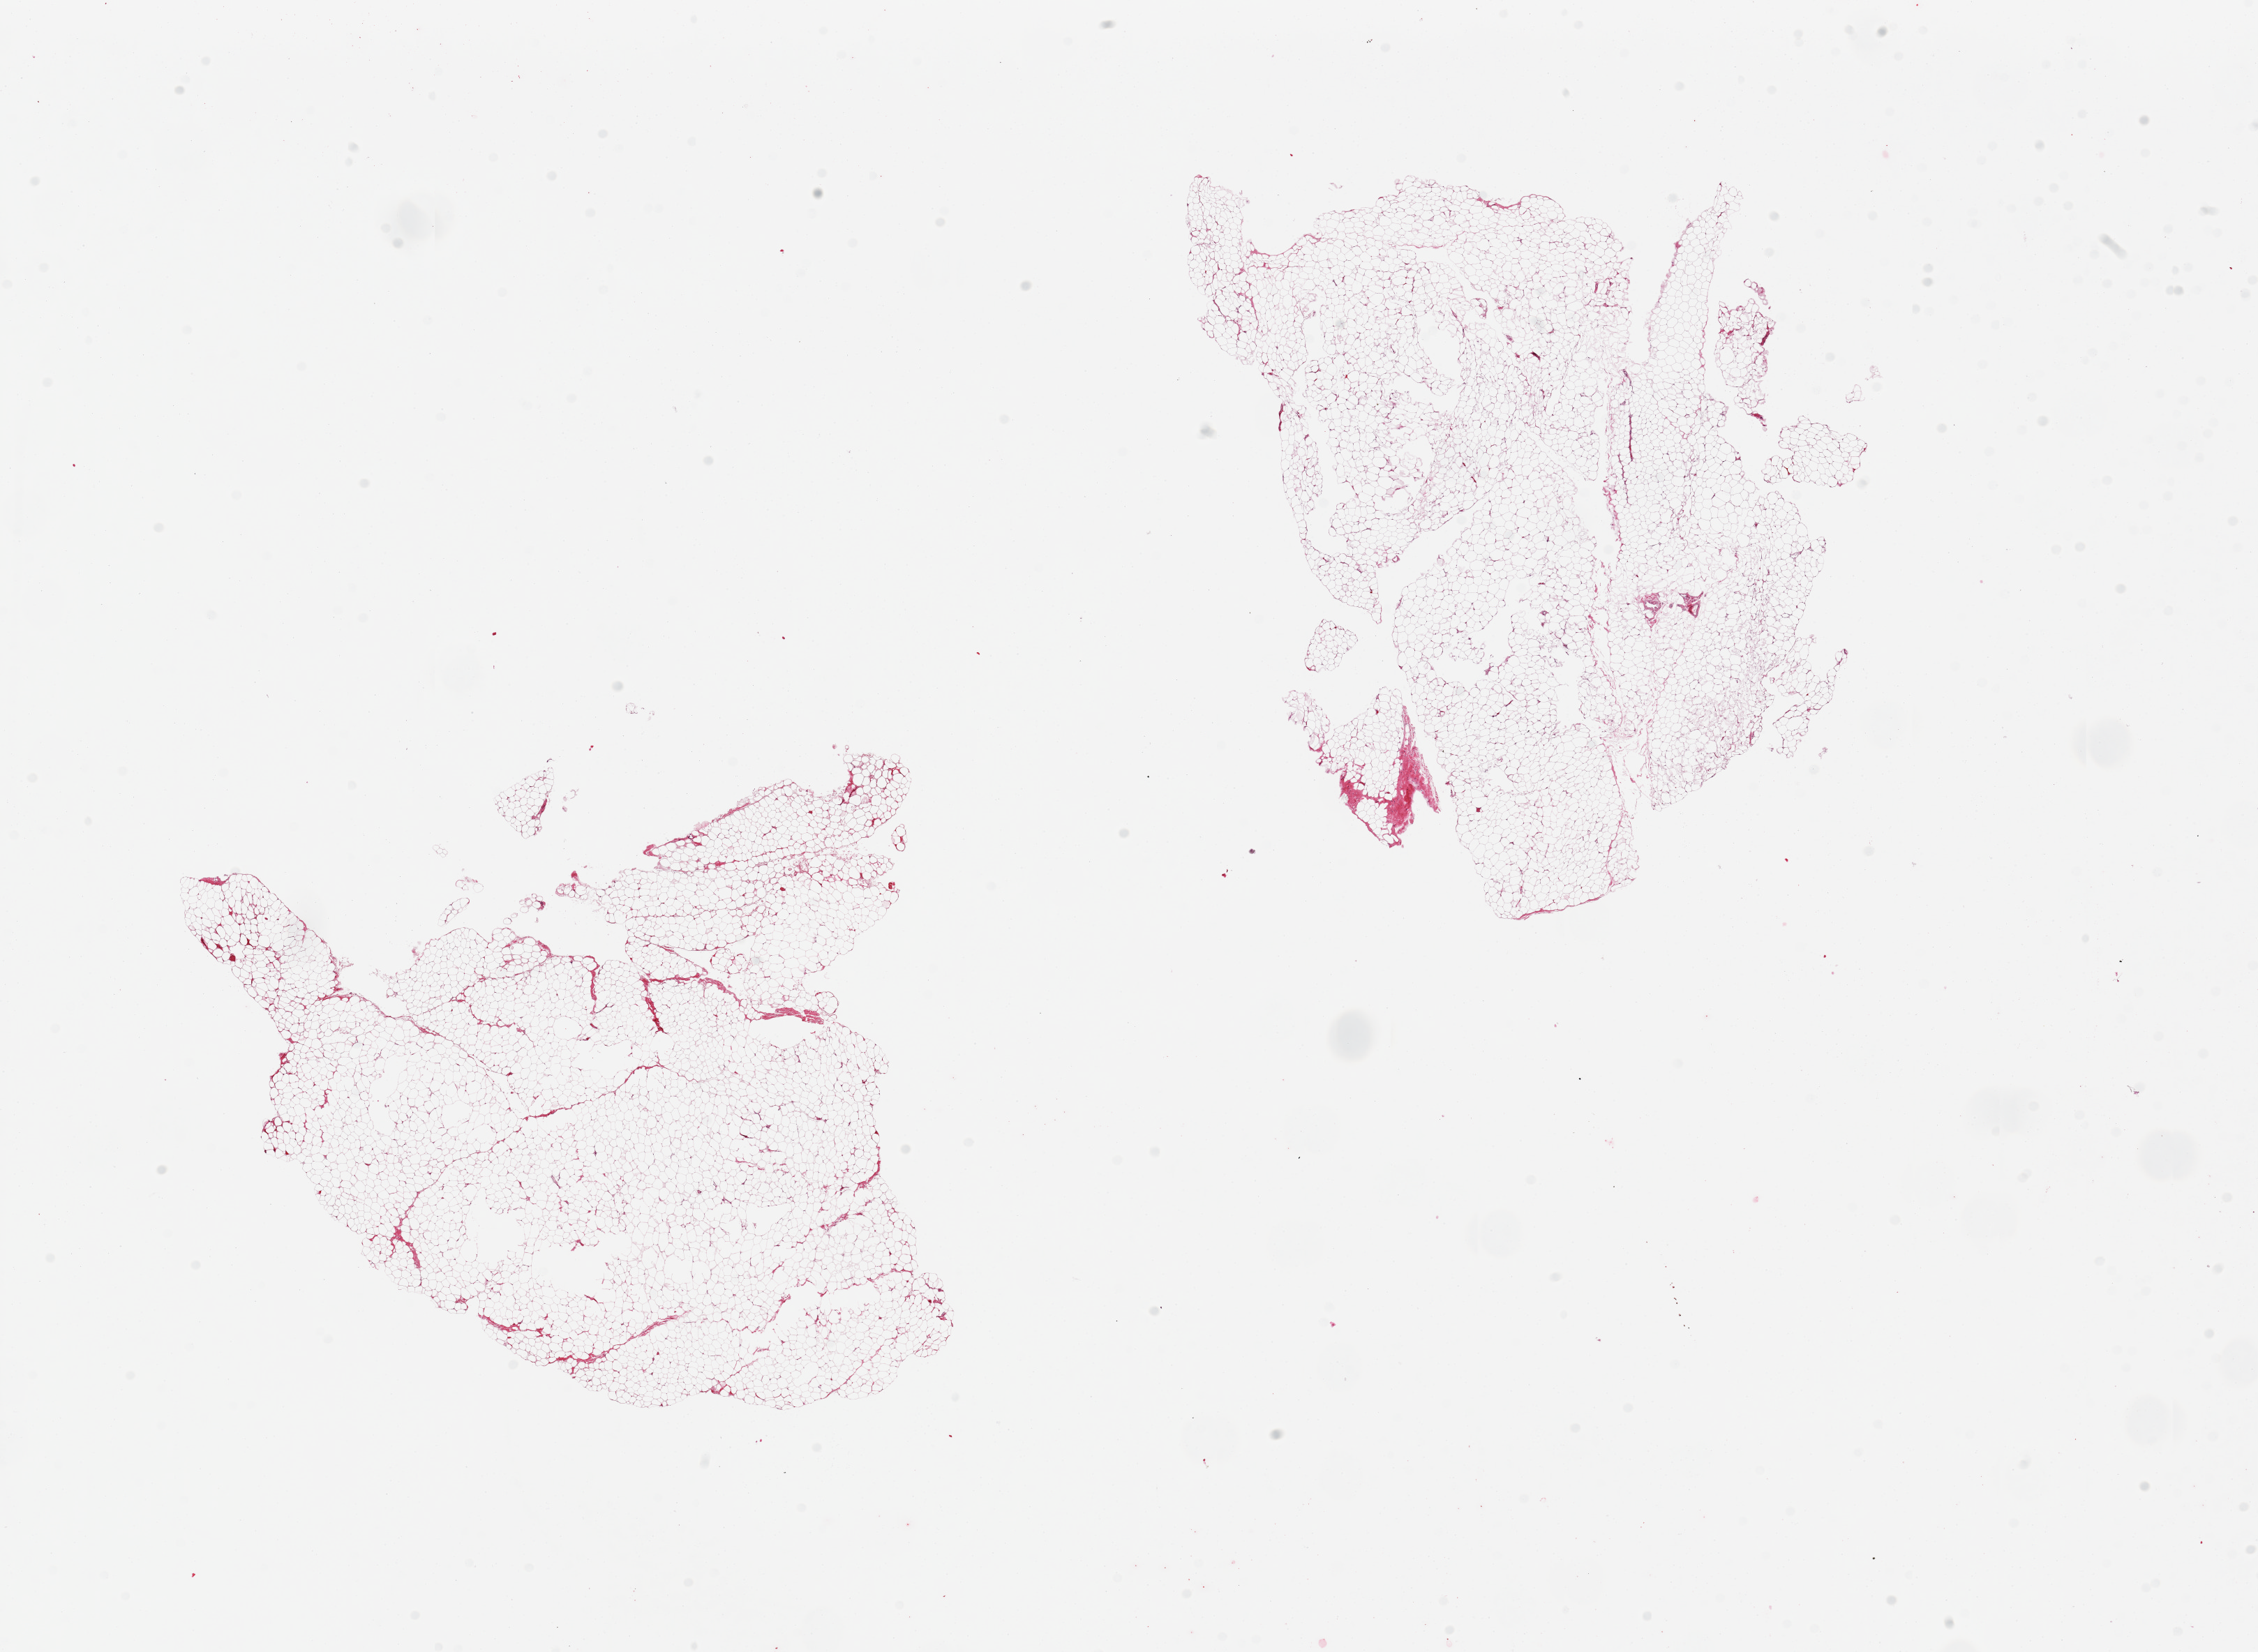
Digitized H&E-stained section — whole scanned area (about 25.6 x 18.7 mm) shown as a low-resolution overview; PAXgene-fixed, paraffin-embedded tissue; section of breast (target tissue); tissue donor sample. Donor: male.
Review note (as recorded): 2 pieces all adipose tissue, no ductal/lobular elements.